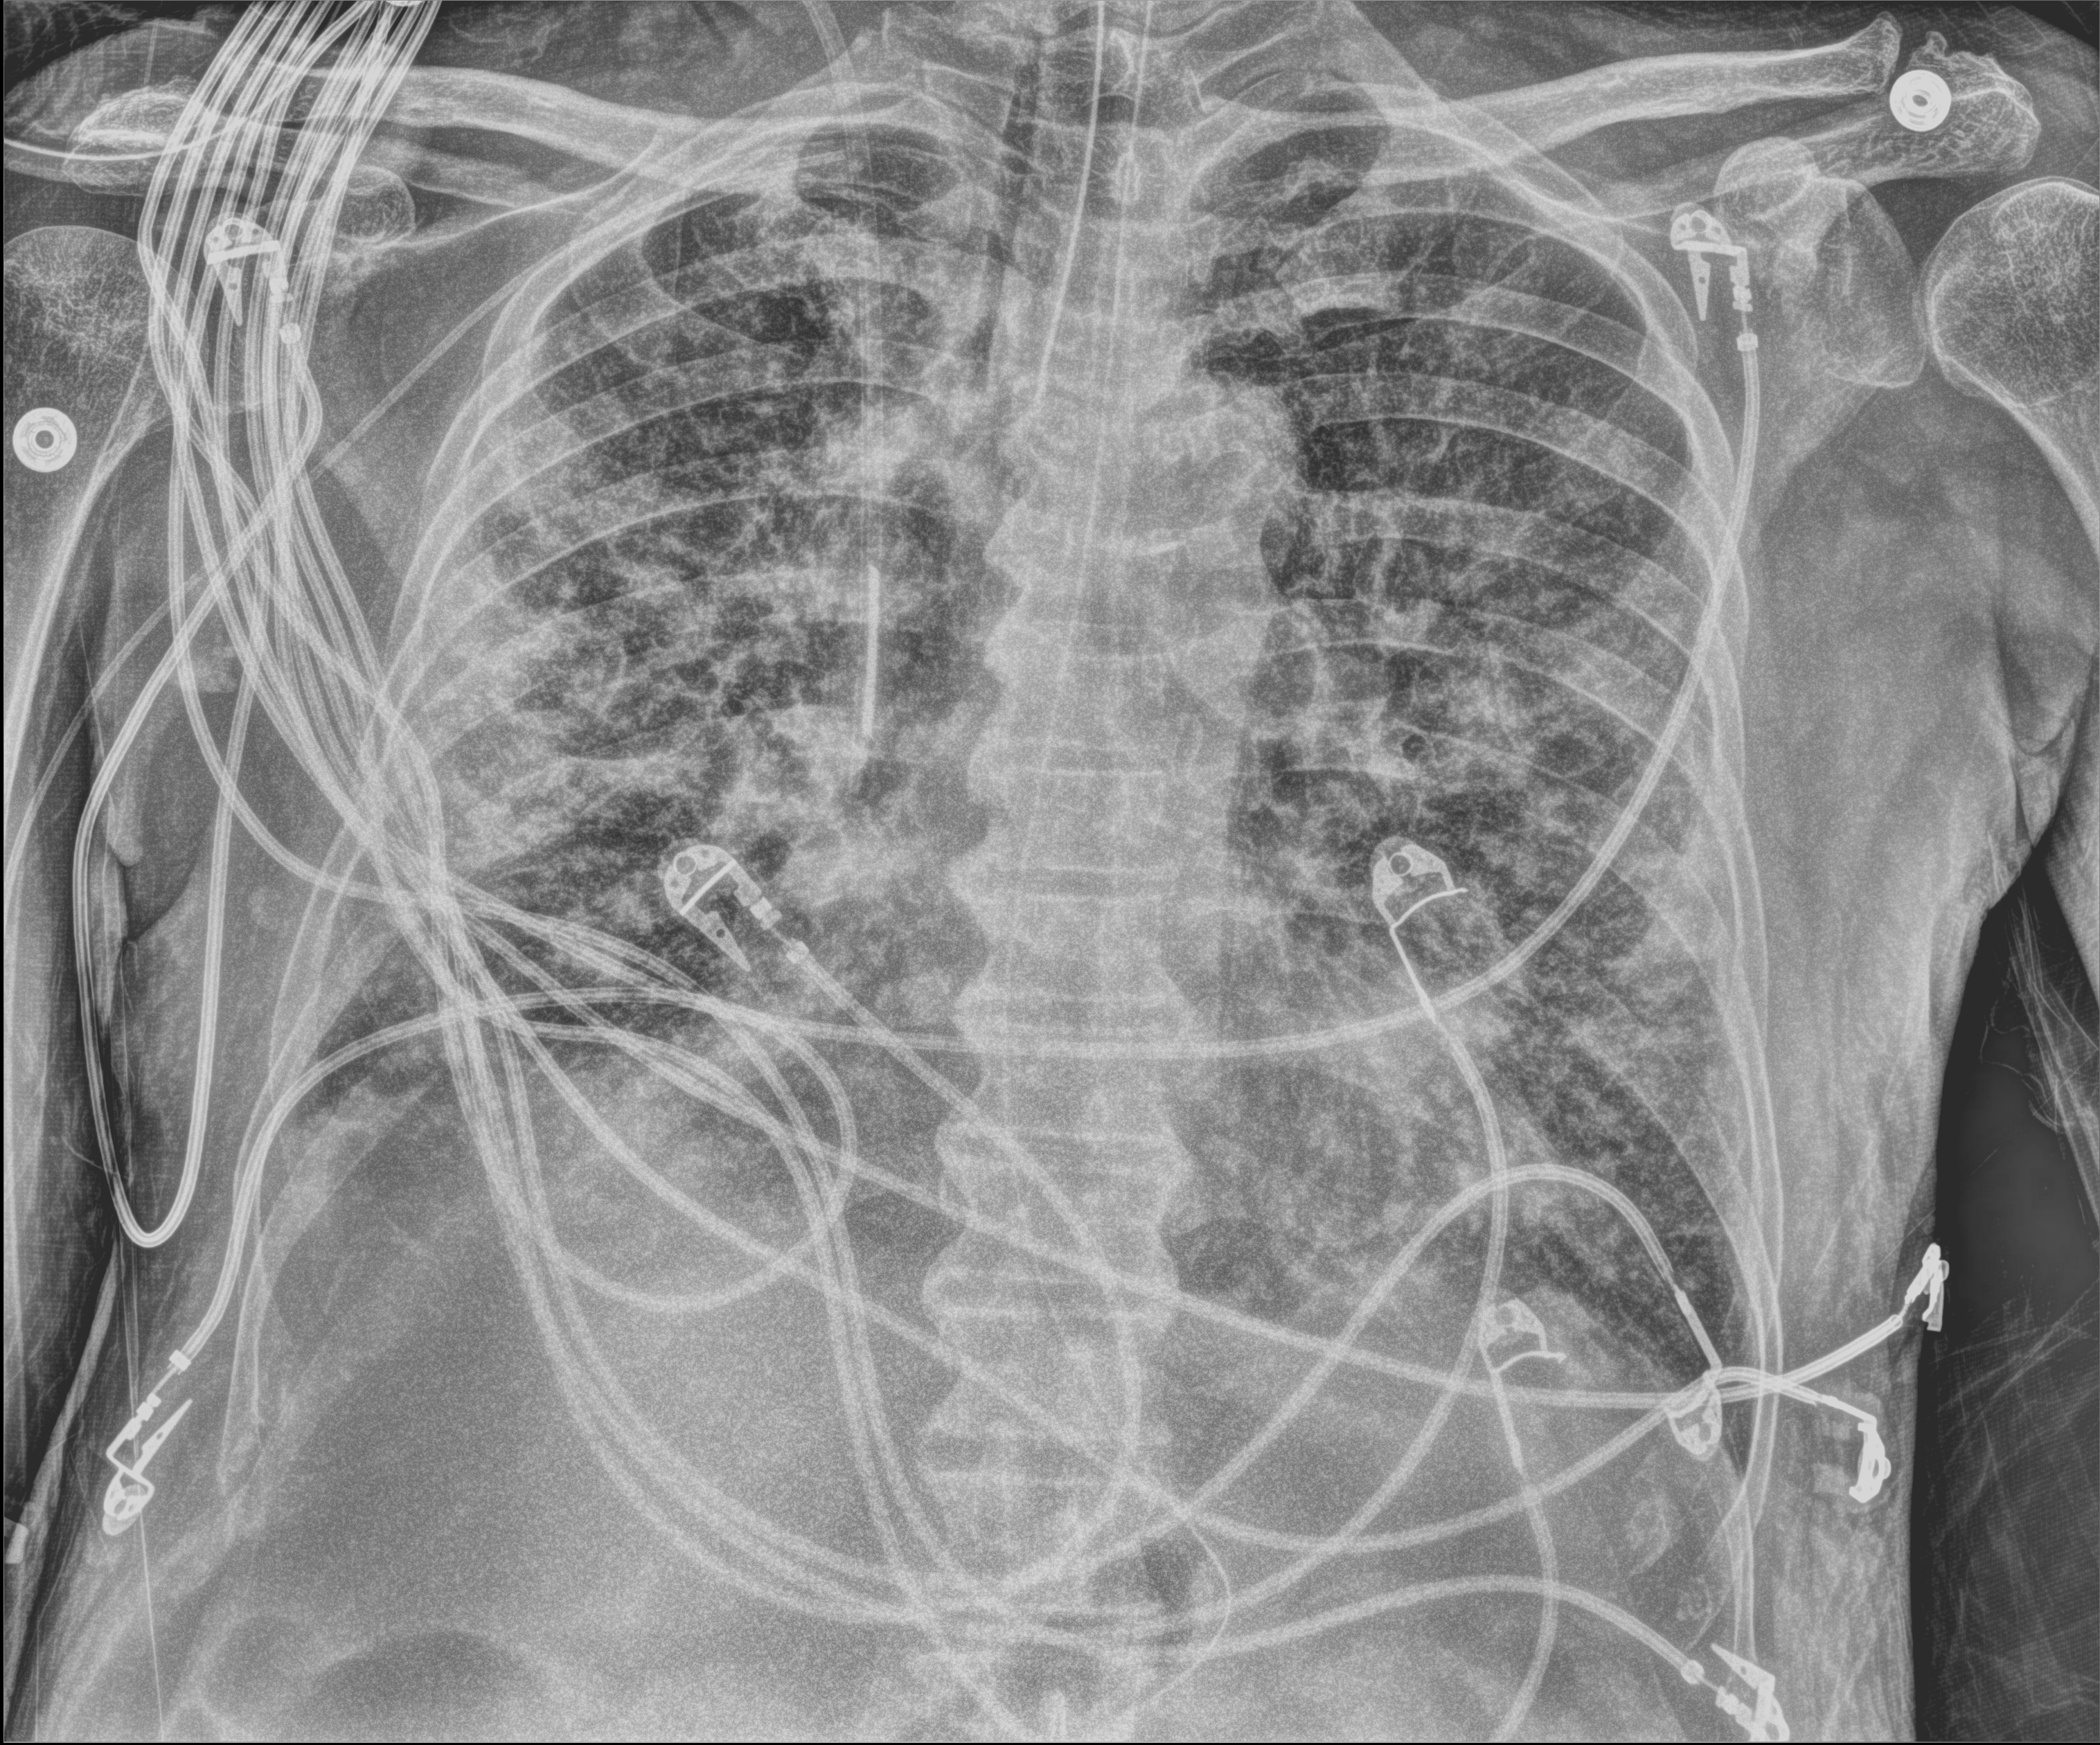
Portable chest radiograph, anteroposterior (AP) projection. Male patient hospitalised with COVID-19, age 60–74 years.
Admission-level facts for this patient (not findings on this image; timing relative to this image not recorded): other chronic lung disease (admission record): no; admitted to intensive care during this hospital stay: yes.